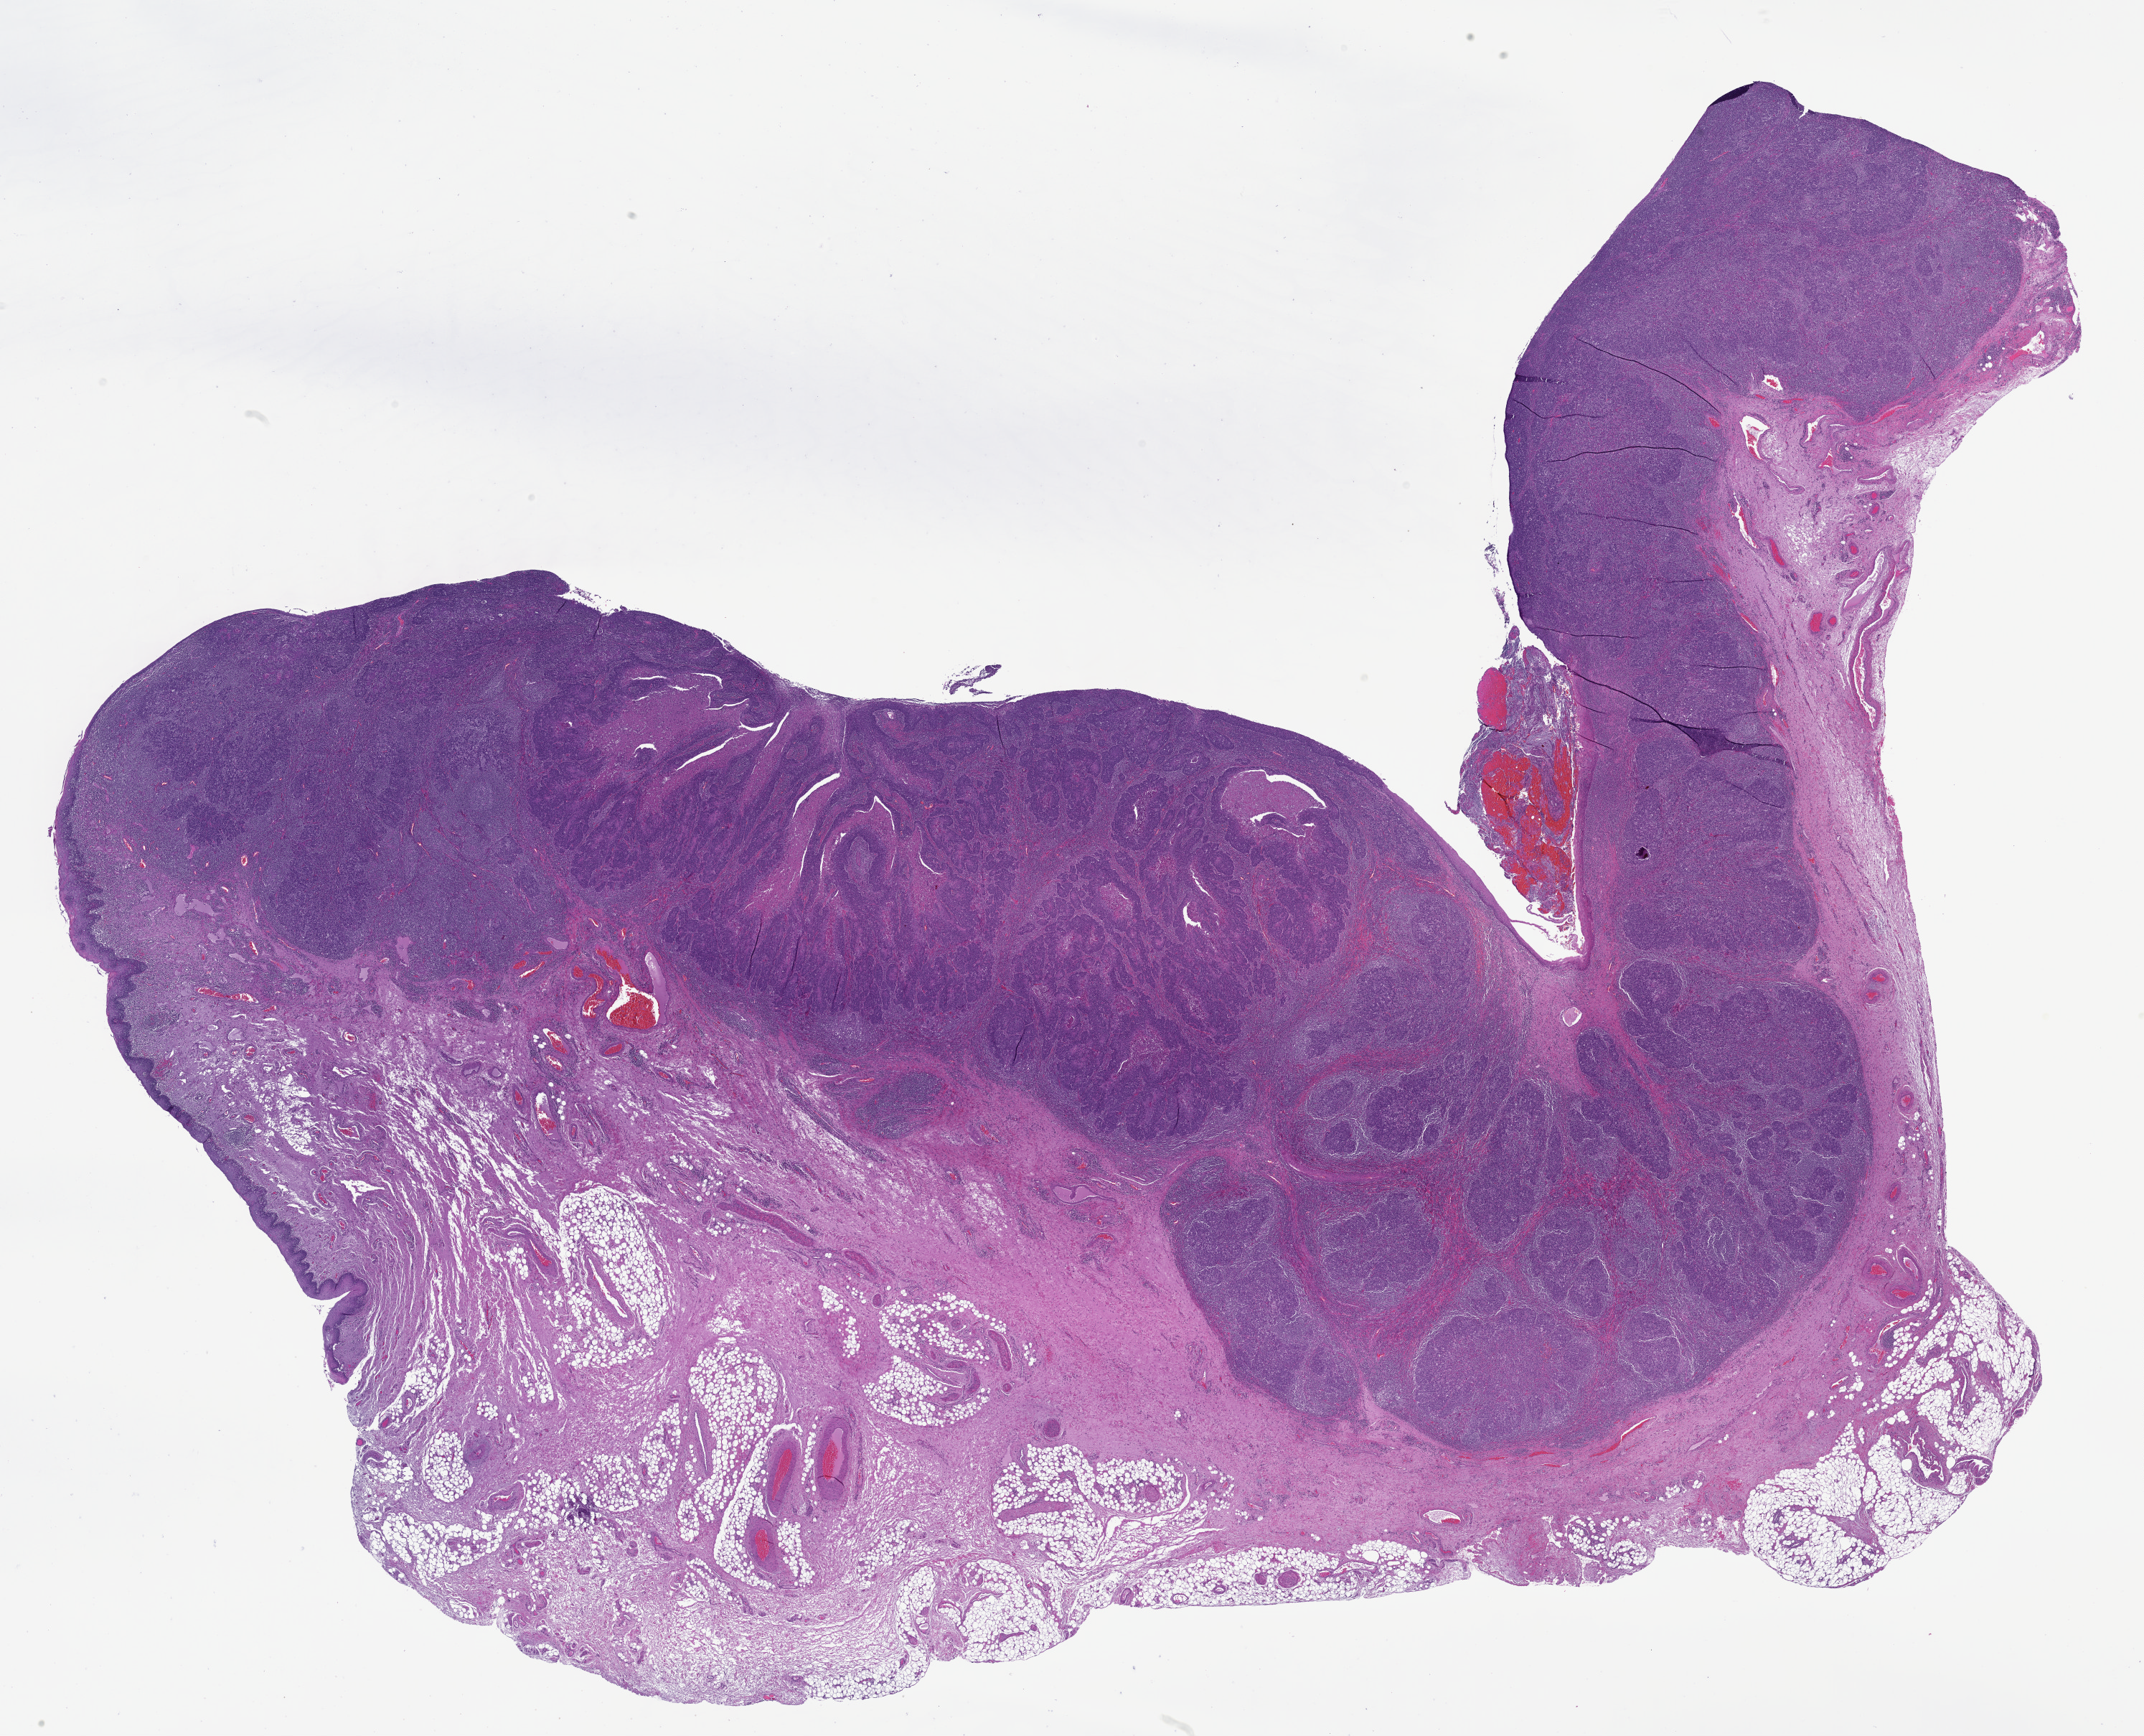
Digitized H&E tissue section (whole slide) — low-resolution overview of the scanned area, about 24.1 x 19.5 mm (acquisition: 40x scan), formalin-fixed paraffin-embedded (FFPE) diagnostic section, head and neck, primary tumour sample. Male patient; age at initial diagnosis 63 years. Histologic grade: G3 (poorly differentiated).
TNM: T3 N0. Pathologic diagnosis: Squamous cell carcinoma, NOS (larynx, NOS). AJCC pathologic stage: III (7th edition).